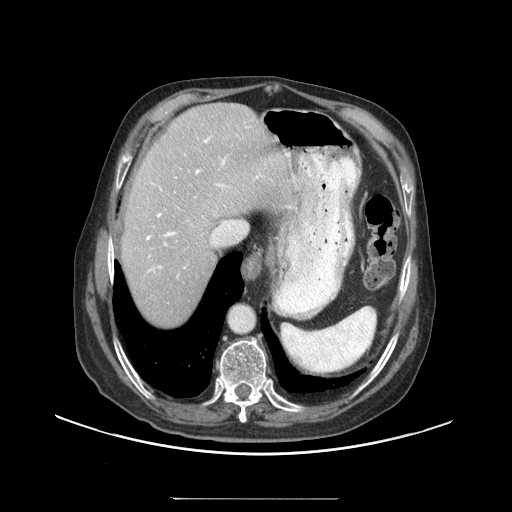
Contrast-enhanced abdominal CT (liver protocol), one axial slice; reconstruction kernel STANDARD; soft-tissue window (W 400 / L 40 HU); 2.5 mm slice thickness; 512 × 512 image matrix, field of view 450 × 450 mm. From the clinical record (not read from this slice): diagnosis: hepatocellular carcinoma (patient treated with transarterial chemoembolisation; whether this scan precedes or follows treatment is not stated here); TNM stage (as recorded): Stage-IIIC; Child-Pugh class: A; tumour differentiation: well differentiated; tumour nodularity: uninodular.
Outlined on this slice (semi-automatic segmentation, software-assisted and operator-edited):
- abdominal aorta: bounding box <230,304,256,332> (left, top, right, bottom; pixels)
- liver parenchyma outside the tumour (the mass and vessels are separate outlines, so this box may not span the whole liver): <122,102,291,324>
- liver vessels: <146,126,262,277>